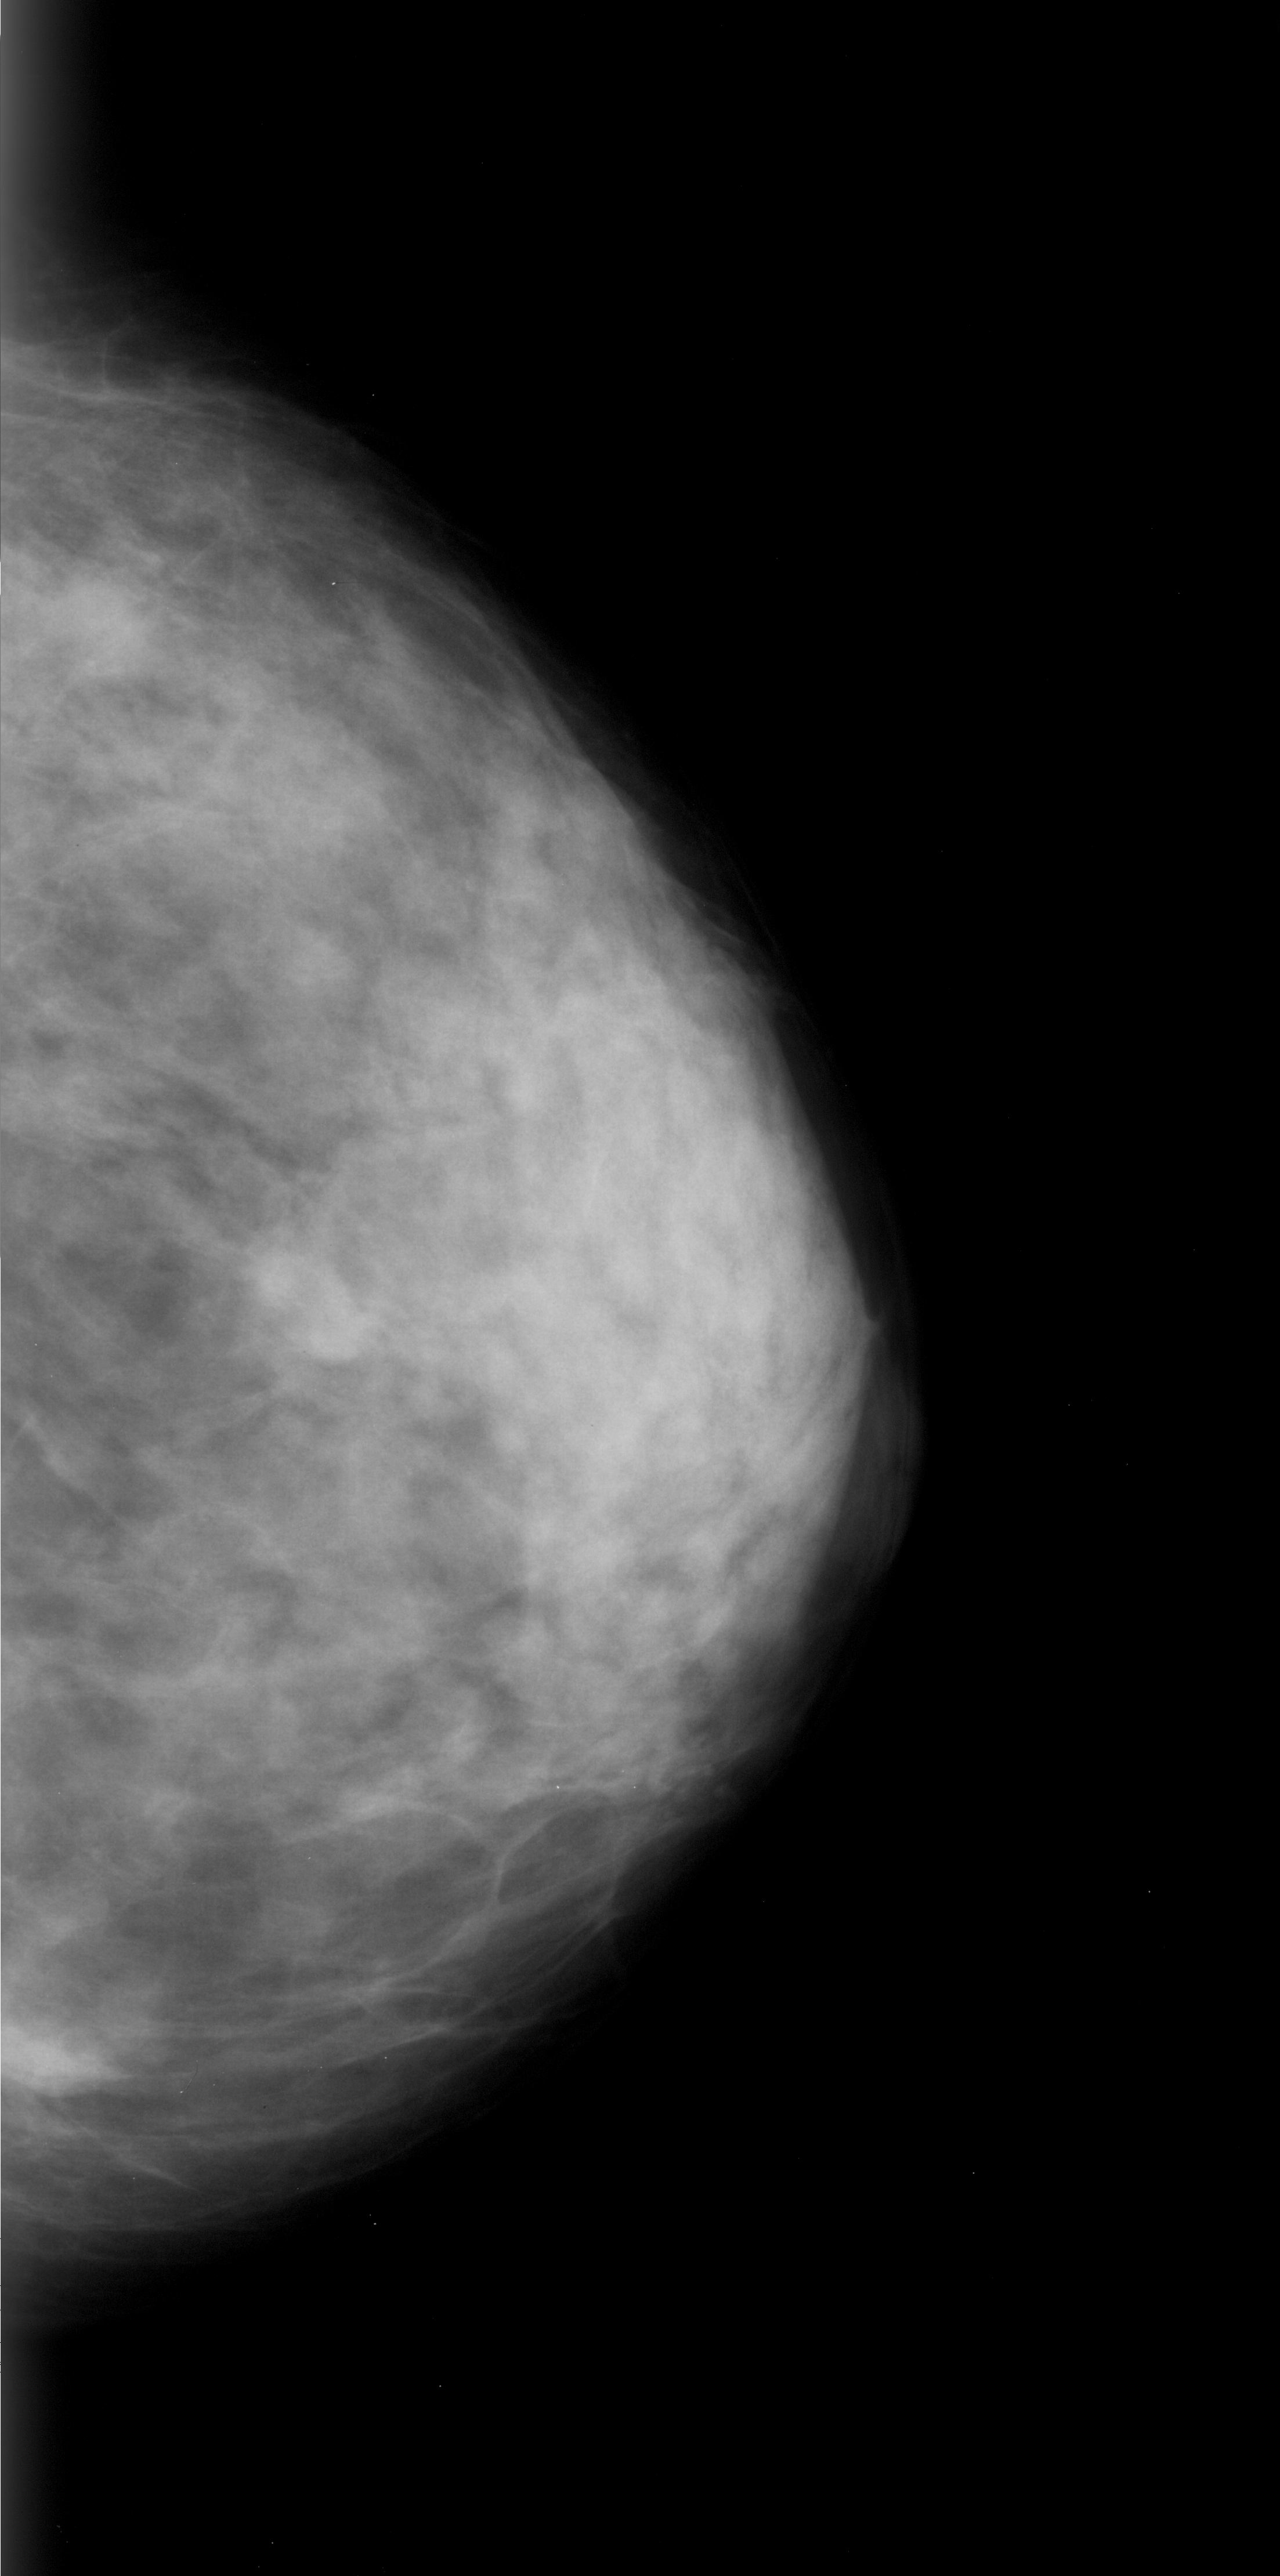
Scanned film-screen mammogram. Right breast. Craniocaudal (CC) view. 1280 × 2576 image matrix.
Marked abnormalities (boxes around the expert regions of interest):
- mass, shape oval, margins ill defined; BI-RADS assessment category 4; subtlety rating 4 on a 1 (subtle) to 5 (obvious) scale; pathology (as recorded): malignant: box from (x=281, y=1262) to (x=398, y=1368) px